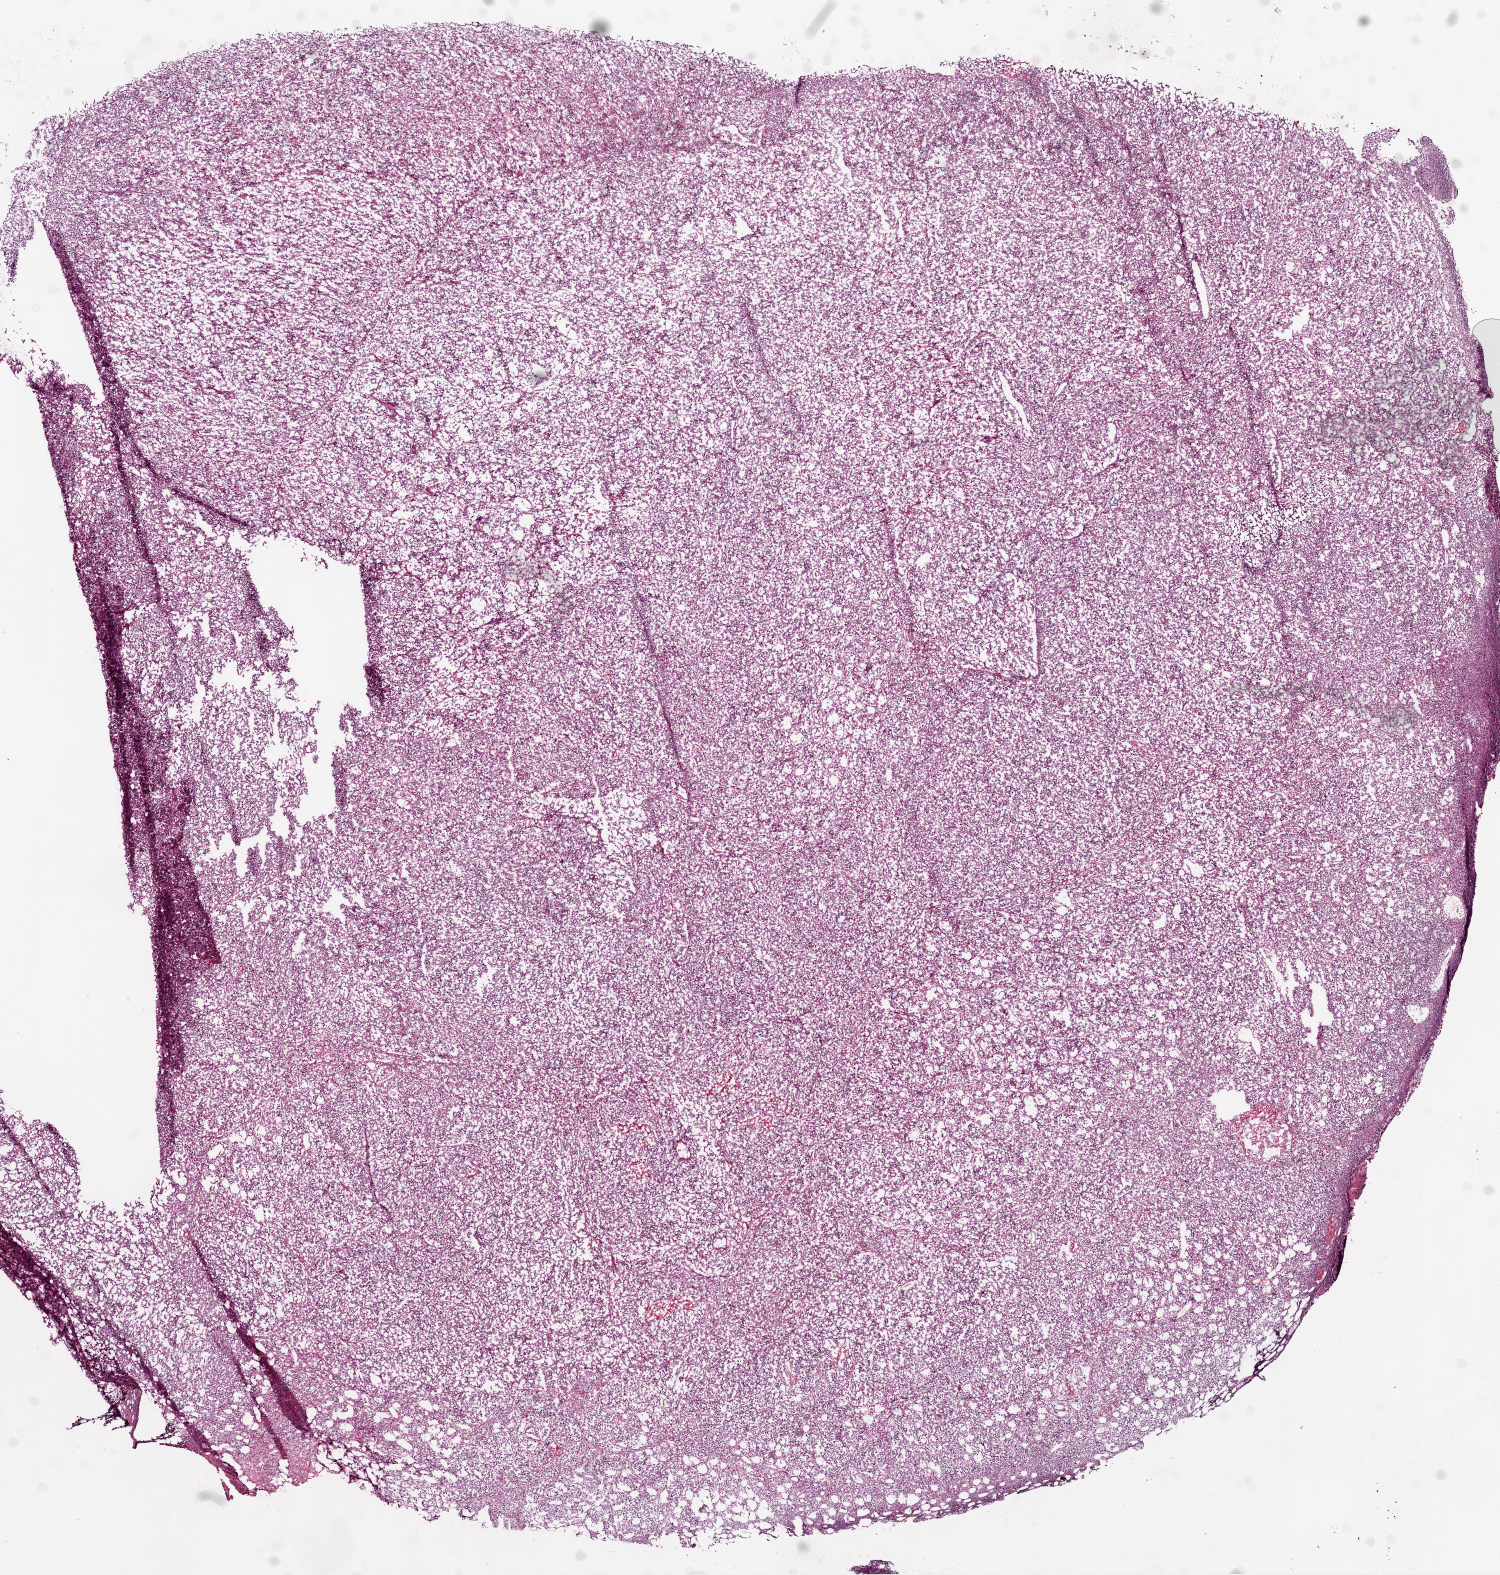
Digitized Hematoxylin and eosin (H&E) stained tissue section (whole slide) — a low-resolution overview of the entire scanned area, about 12.0 x 12.6 mm. Frozen section from the bottom of the tissue portion. Kidney, primary tumour sample. Male, age 75 years at initial diagnosis. Histologic grade: G4 (undifferentiated). Composition of this section per pathologist review: tumour cells 95%, tumour nuclei 90%, normal cells 0%, stromal cells 5%, necrosis 0%.
Lymph nodes positive (case pathology): 0 of 6 examined. Pathologic diagnosis: Clear cell adenocarcinoma, NOS. AJCC pathologic stage: IV.